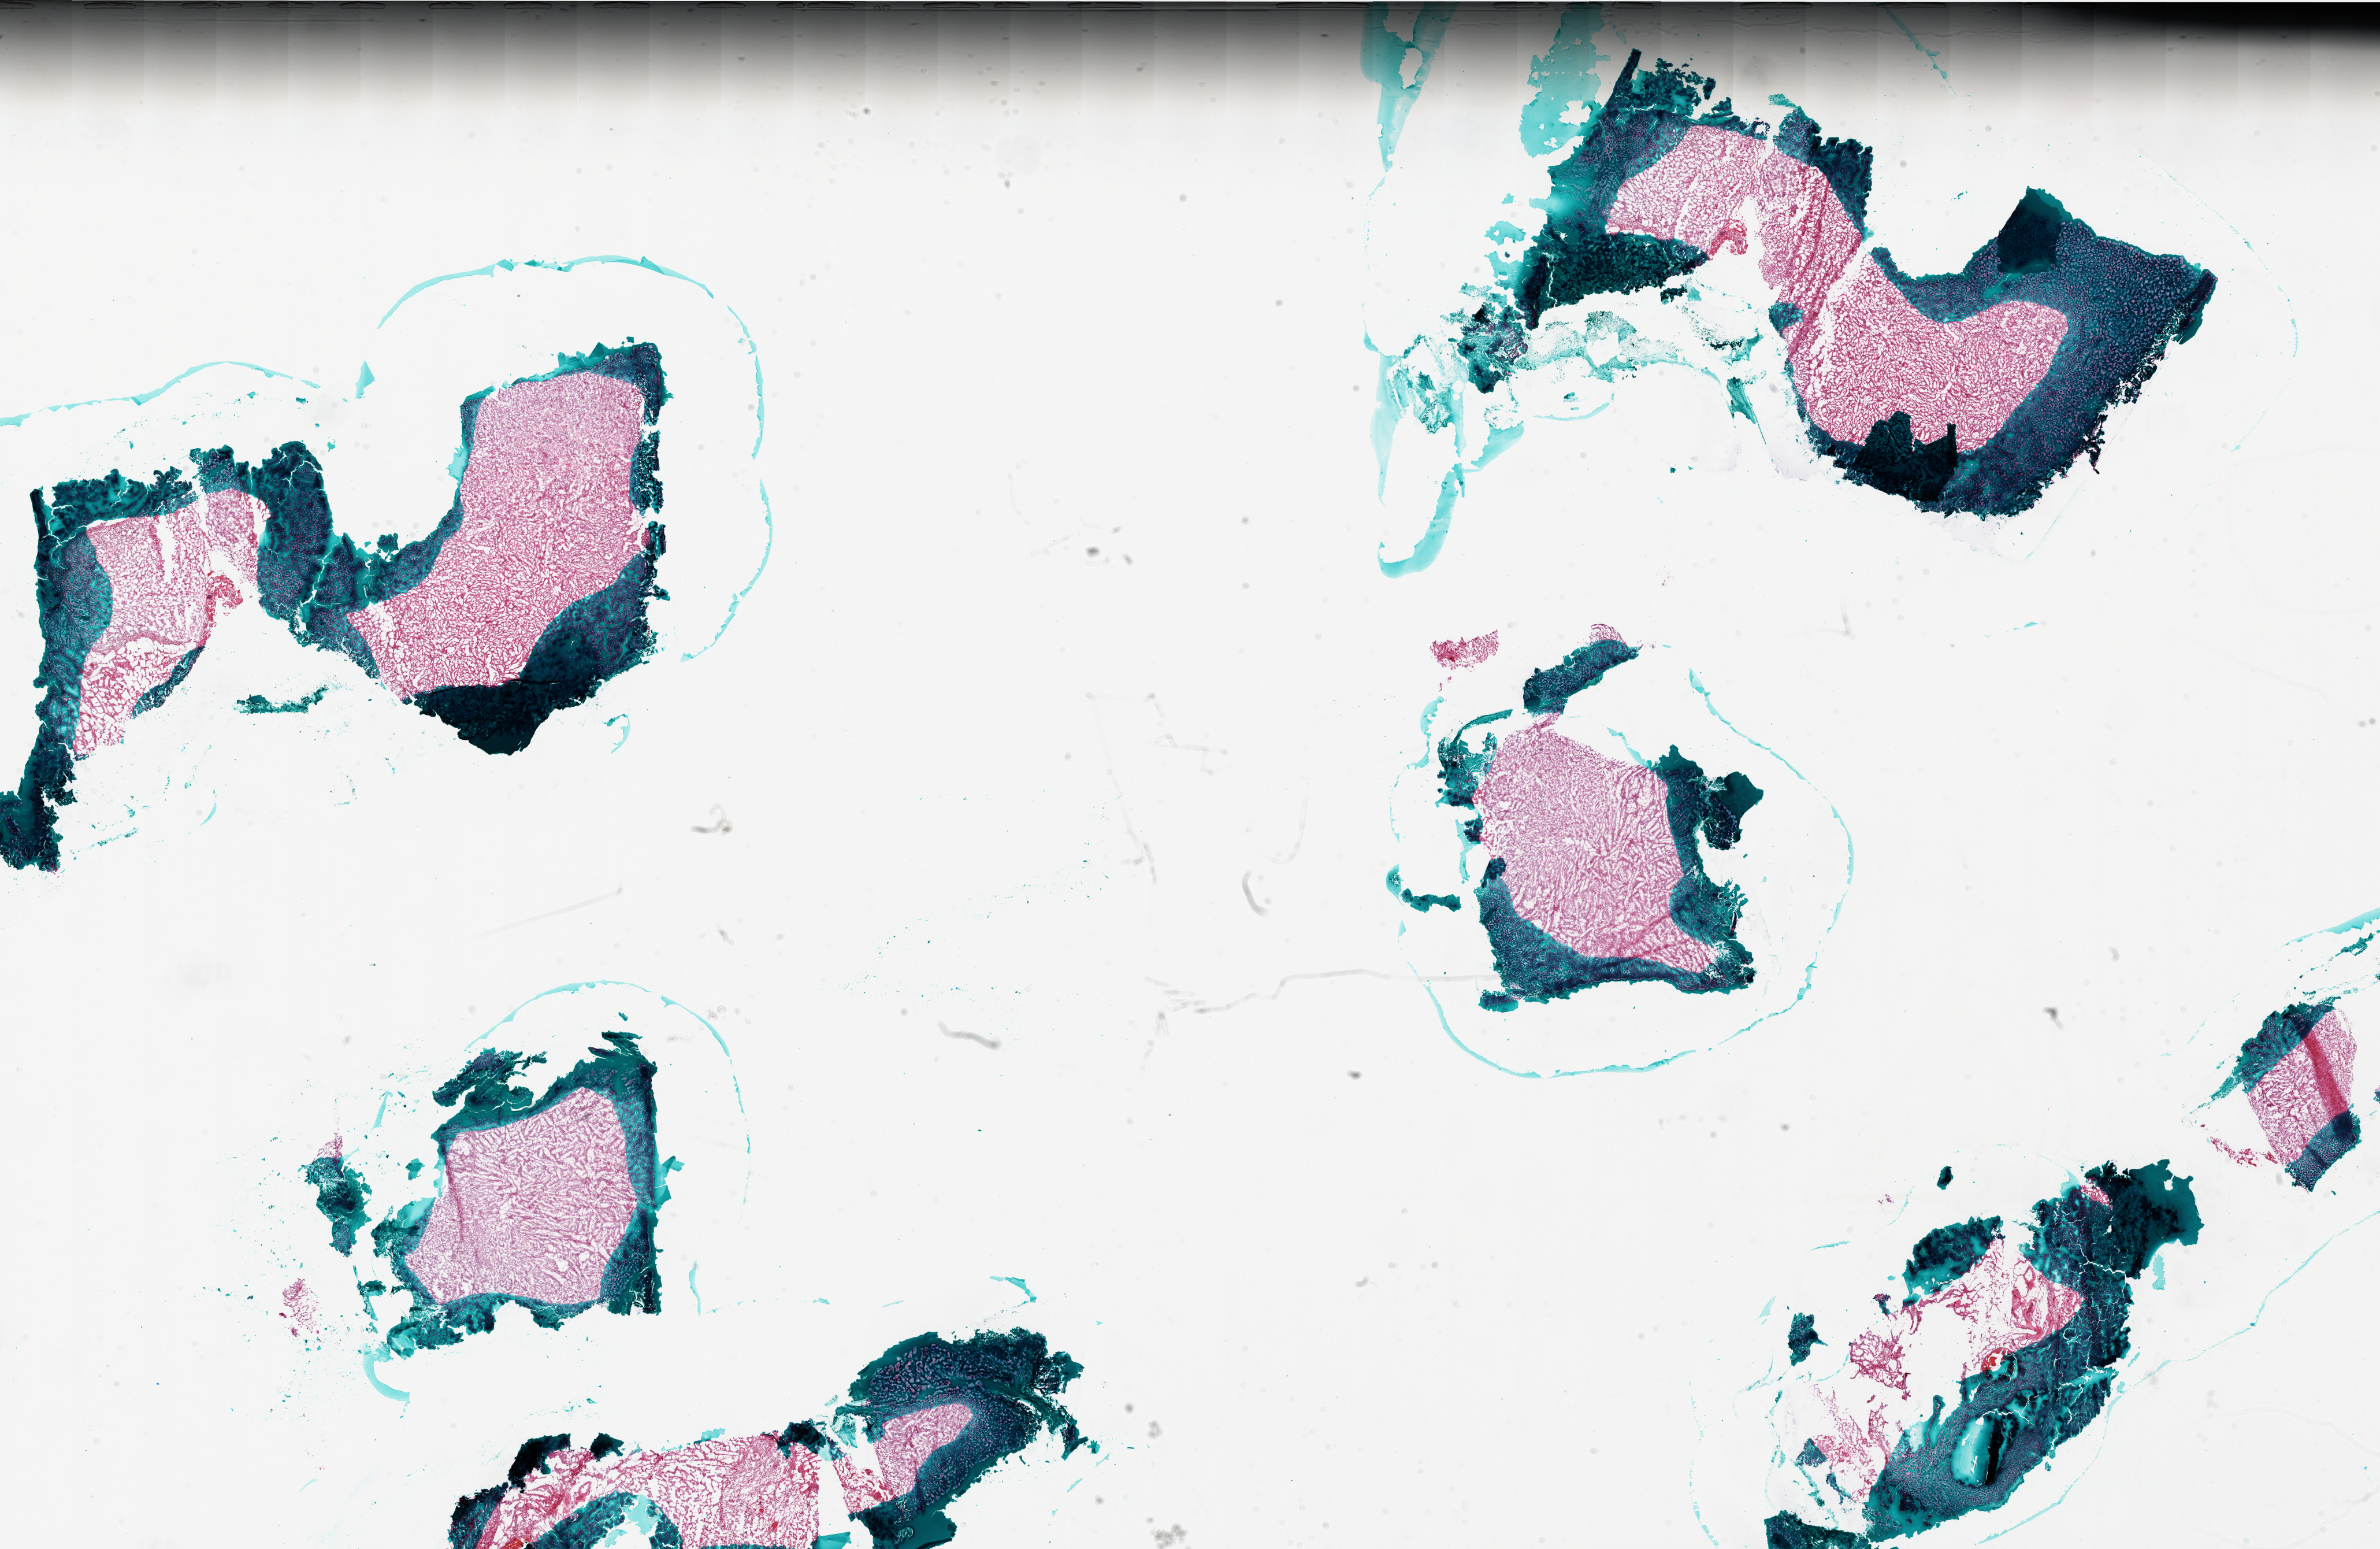
Digitized H&E tissue section (whole slide) — shown as a low-resolution overview of the whole scanned area (about 33.0 x 21.4 mm). Frozen section. Sample: primary tumour, brain. Patient: male, age at initial diagnosis 47 years. Slide review estimates, as recorded: tumour cells 80%, tumour nuclei 100%, normal cells 0%, stromal cells 0%, necrosis 20%.
Diagnosis: Glioblastoma.